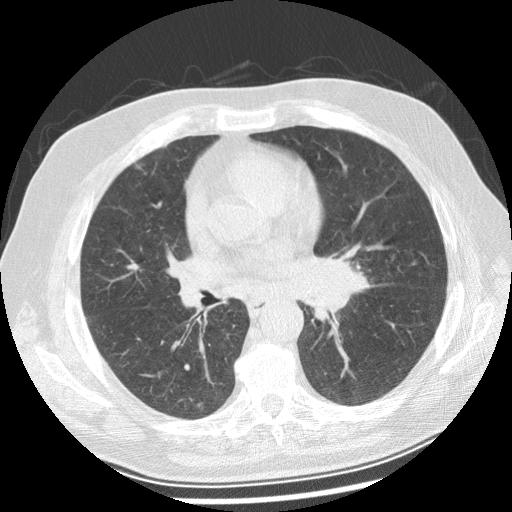
Low-dose screening chest CT, one axial slice. Reconstruction kernel STANDARD. 120 kVp. Lung window (W 1500 / L -600 HU). 2.5 mm slice thickness. 512 × 512 image matrix, field of view 360 × 360 mm.
Structures marked on this image (expert manual segmentation):
- lesion 1 (tumor, left main bronchus): box from (x=308, y=261) to (x=368, y=319) px